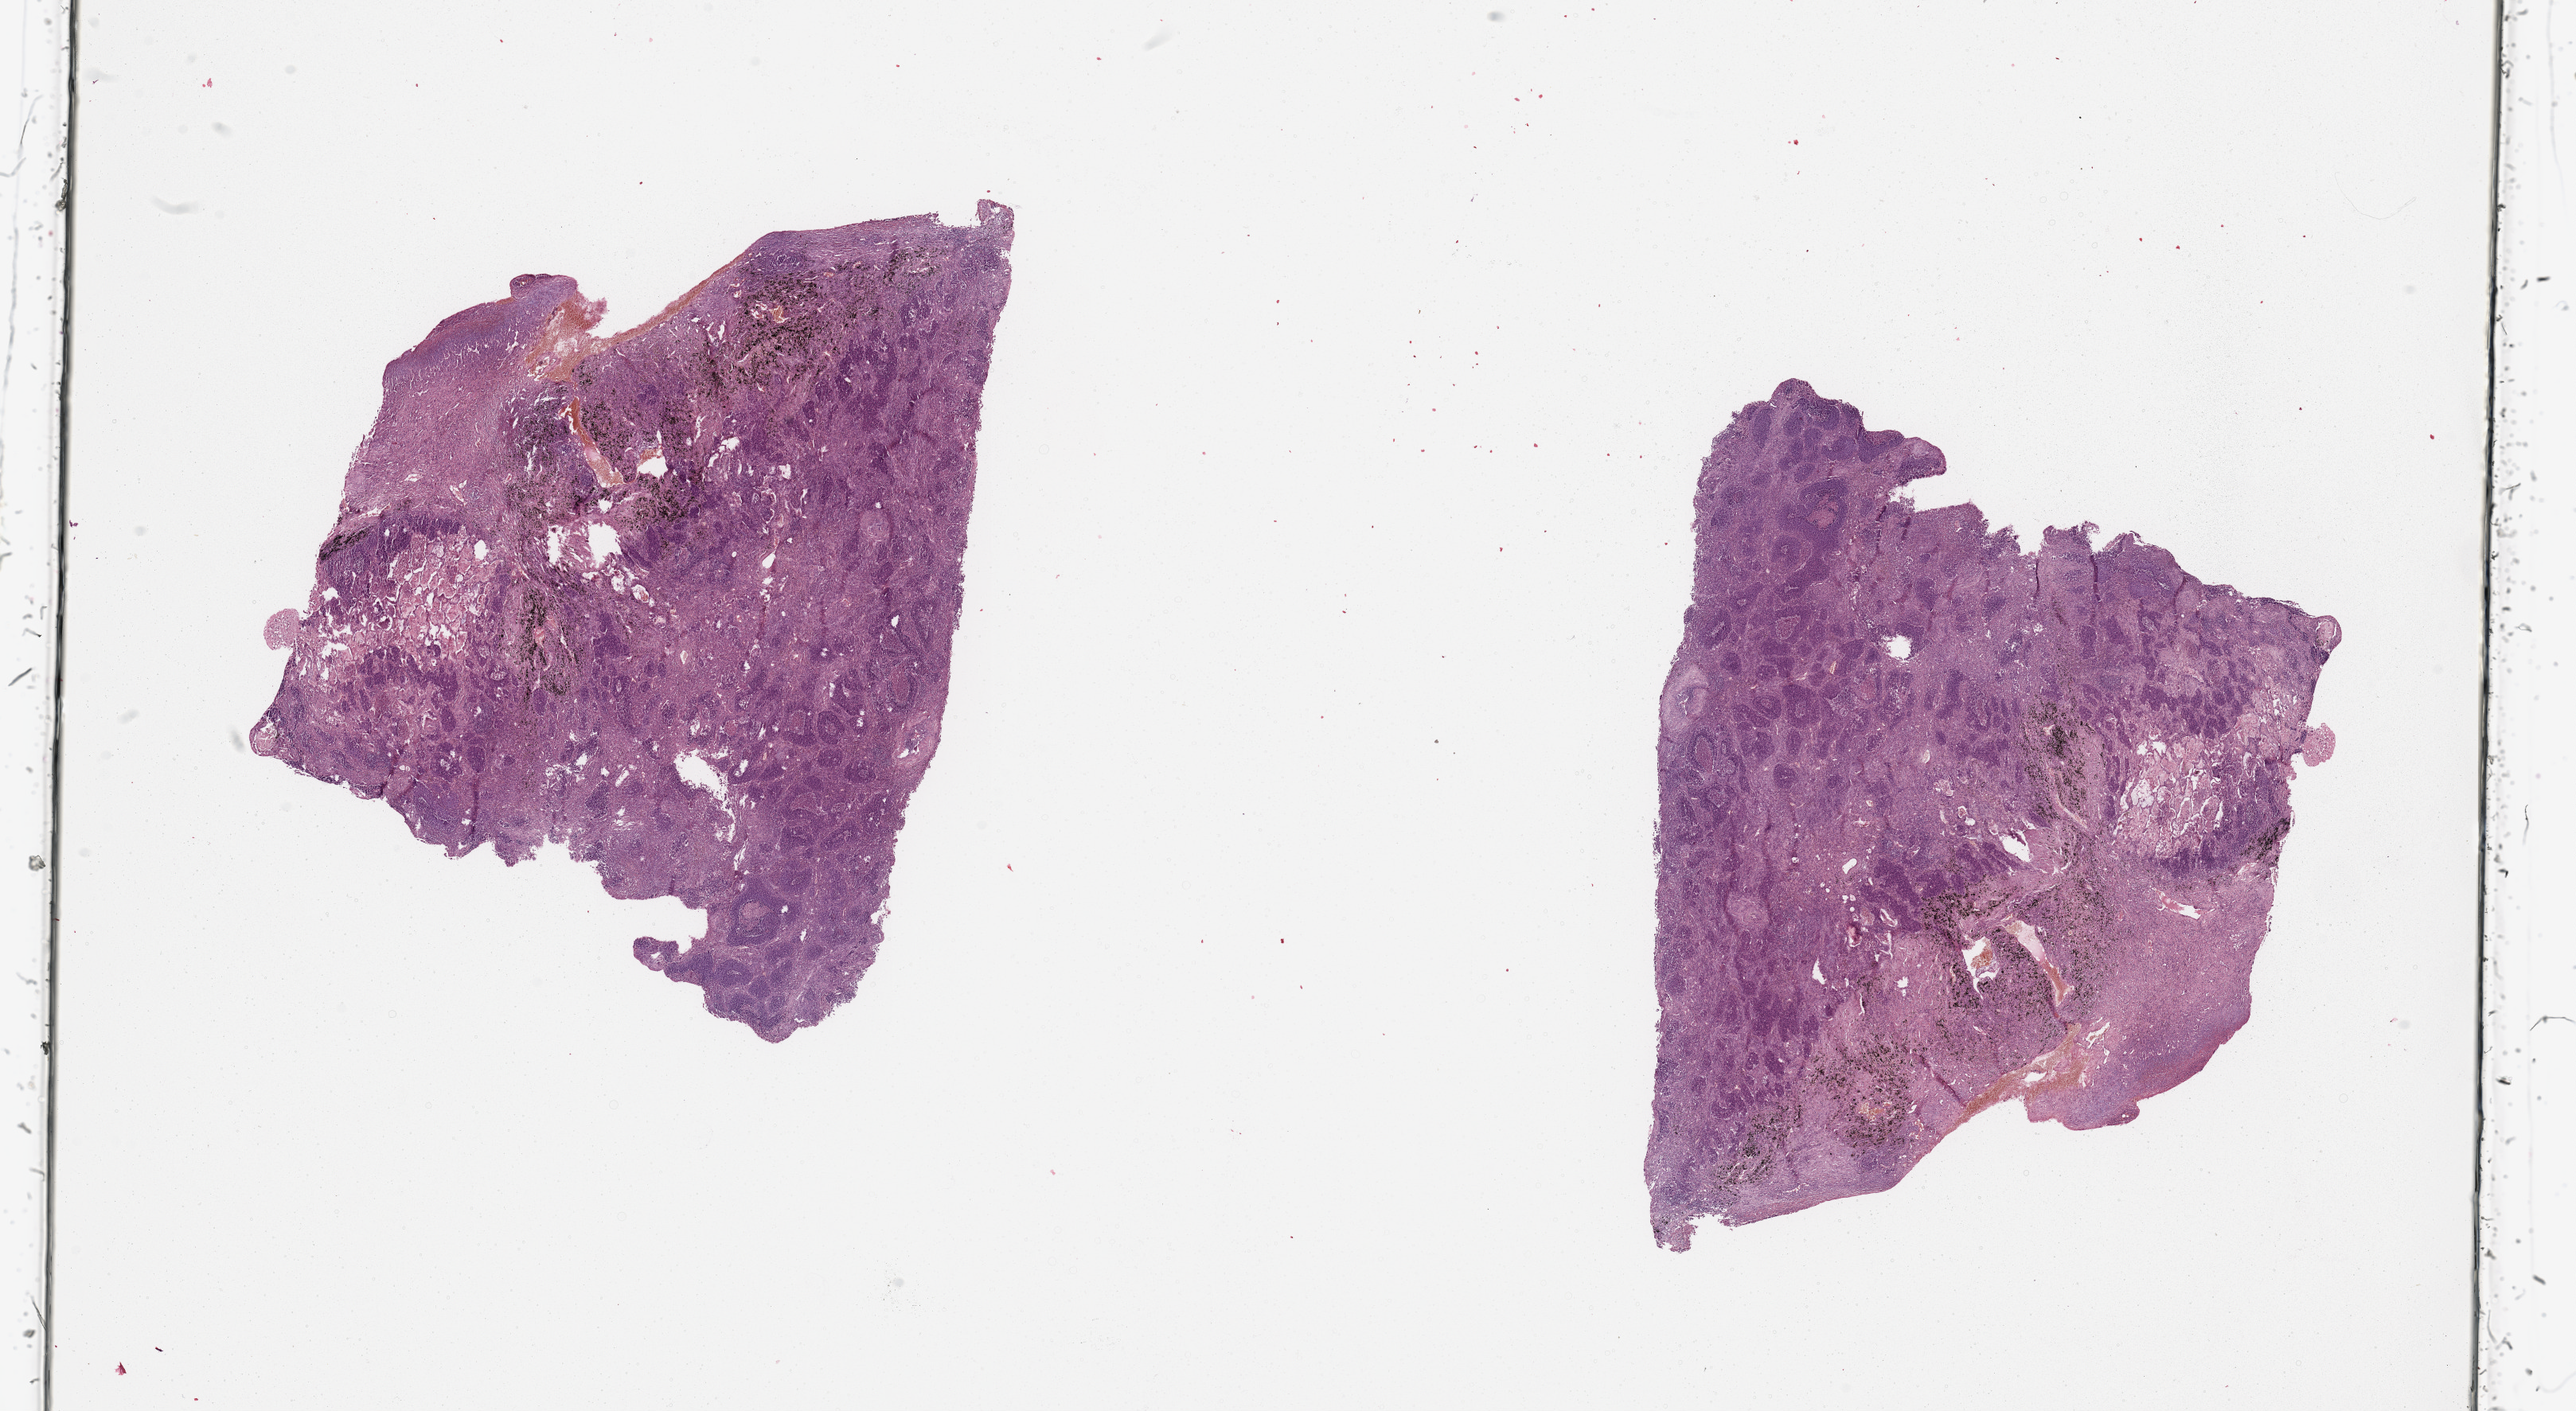
Hematoxylin and eosin (H&E) stained whole-slide image, shown as a low-resolution overview of the whole scanned area (about 25.6 x 14.0 mm). Lung, tumour tissue. 60-year-old male patient. Histologic grade: GX (grade cannot be assessed).
• diagnosis: Squamous cell carcinoma, NOS
• primary tumour site (as recorded): left lower lobe
• AJCC pathologic stage: IB